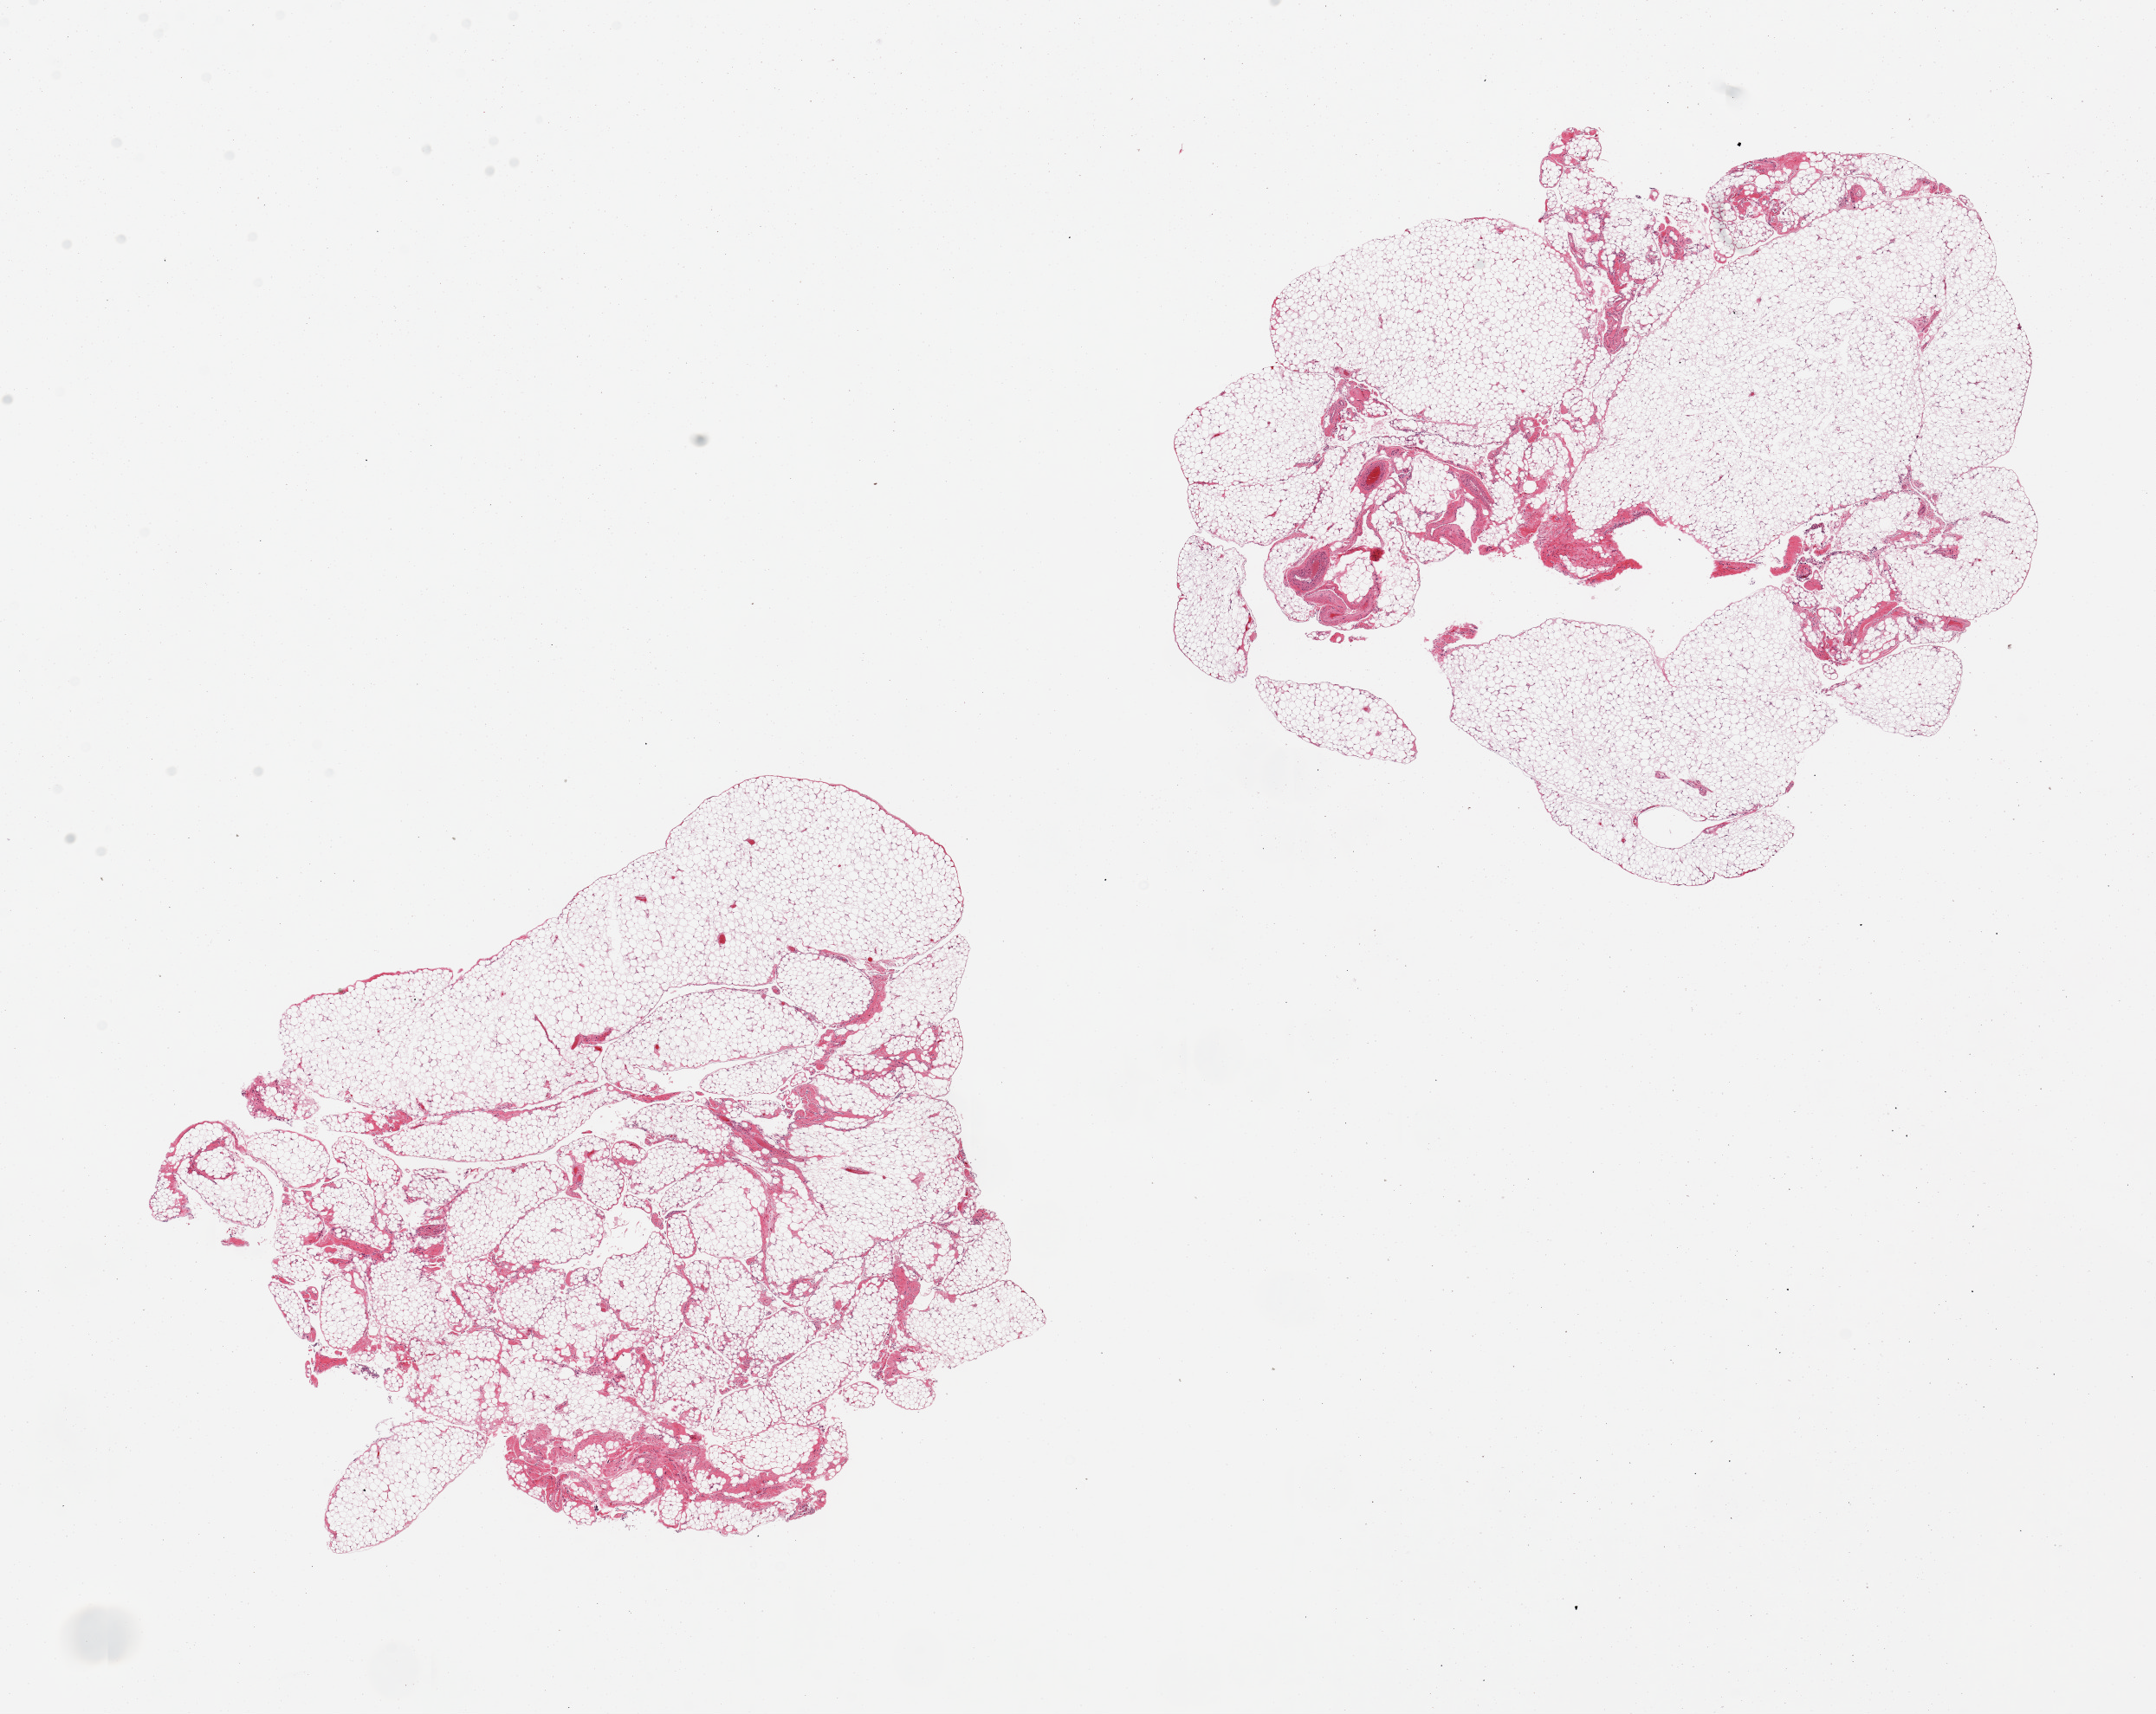
Digitized haematoxylin and eosin-stained section, brightfield — a low-resolution overview of the entire scanned area, about 19.7 x 15.7 mm, PAXgene-fixed, paraffin-embedded tissue, sampled site (target tissue): omentum, tissue donor sample.
Pathologist's review note for this sample: 2 pieces, ~10-15% fascia/vascular tissue.